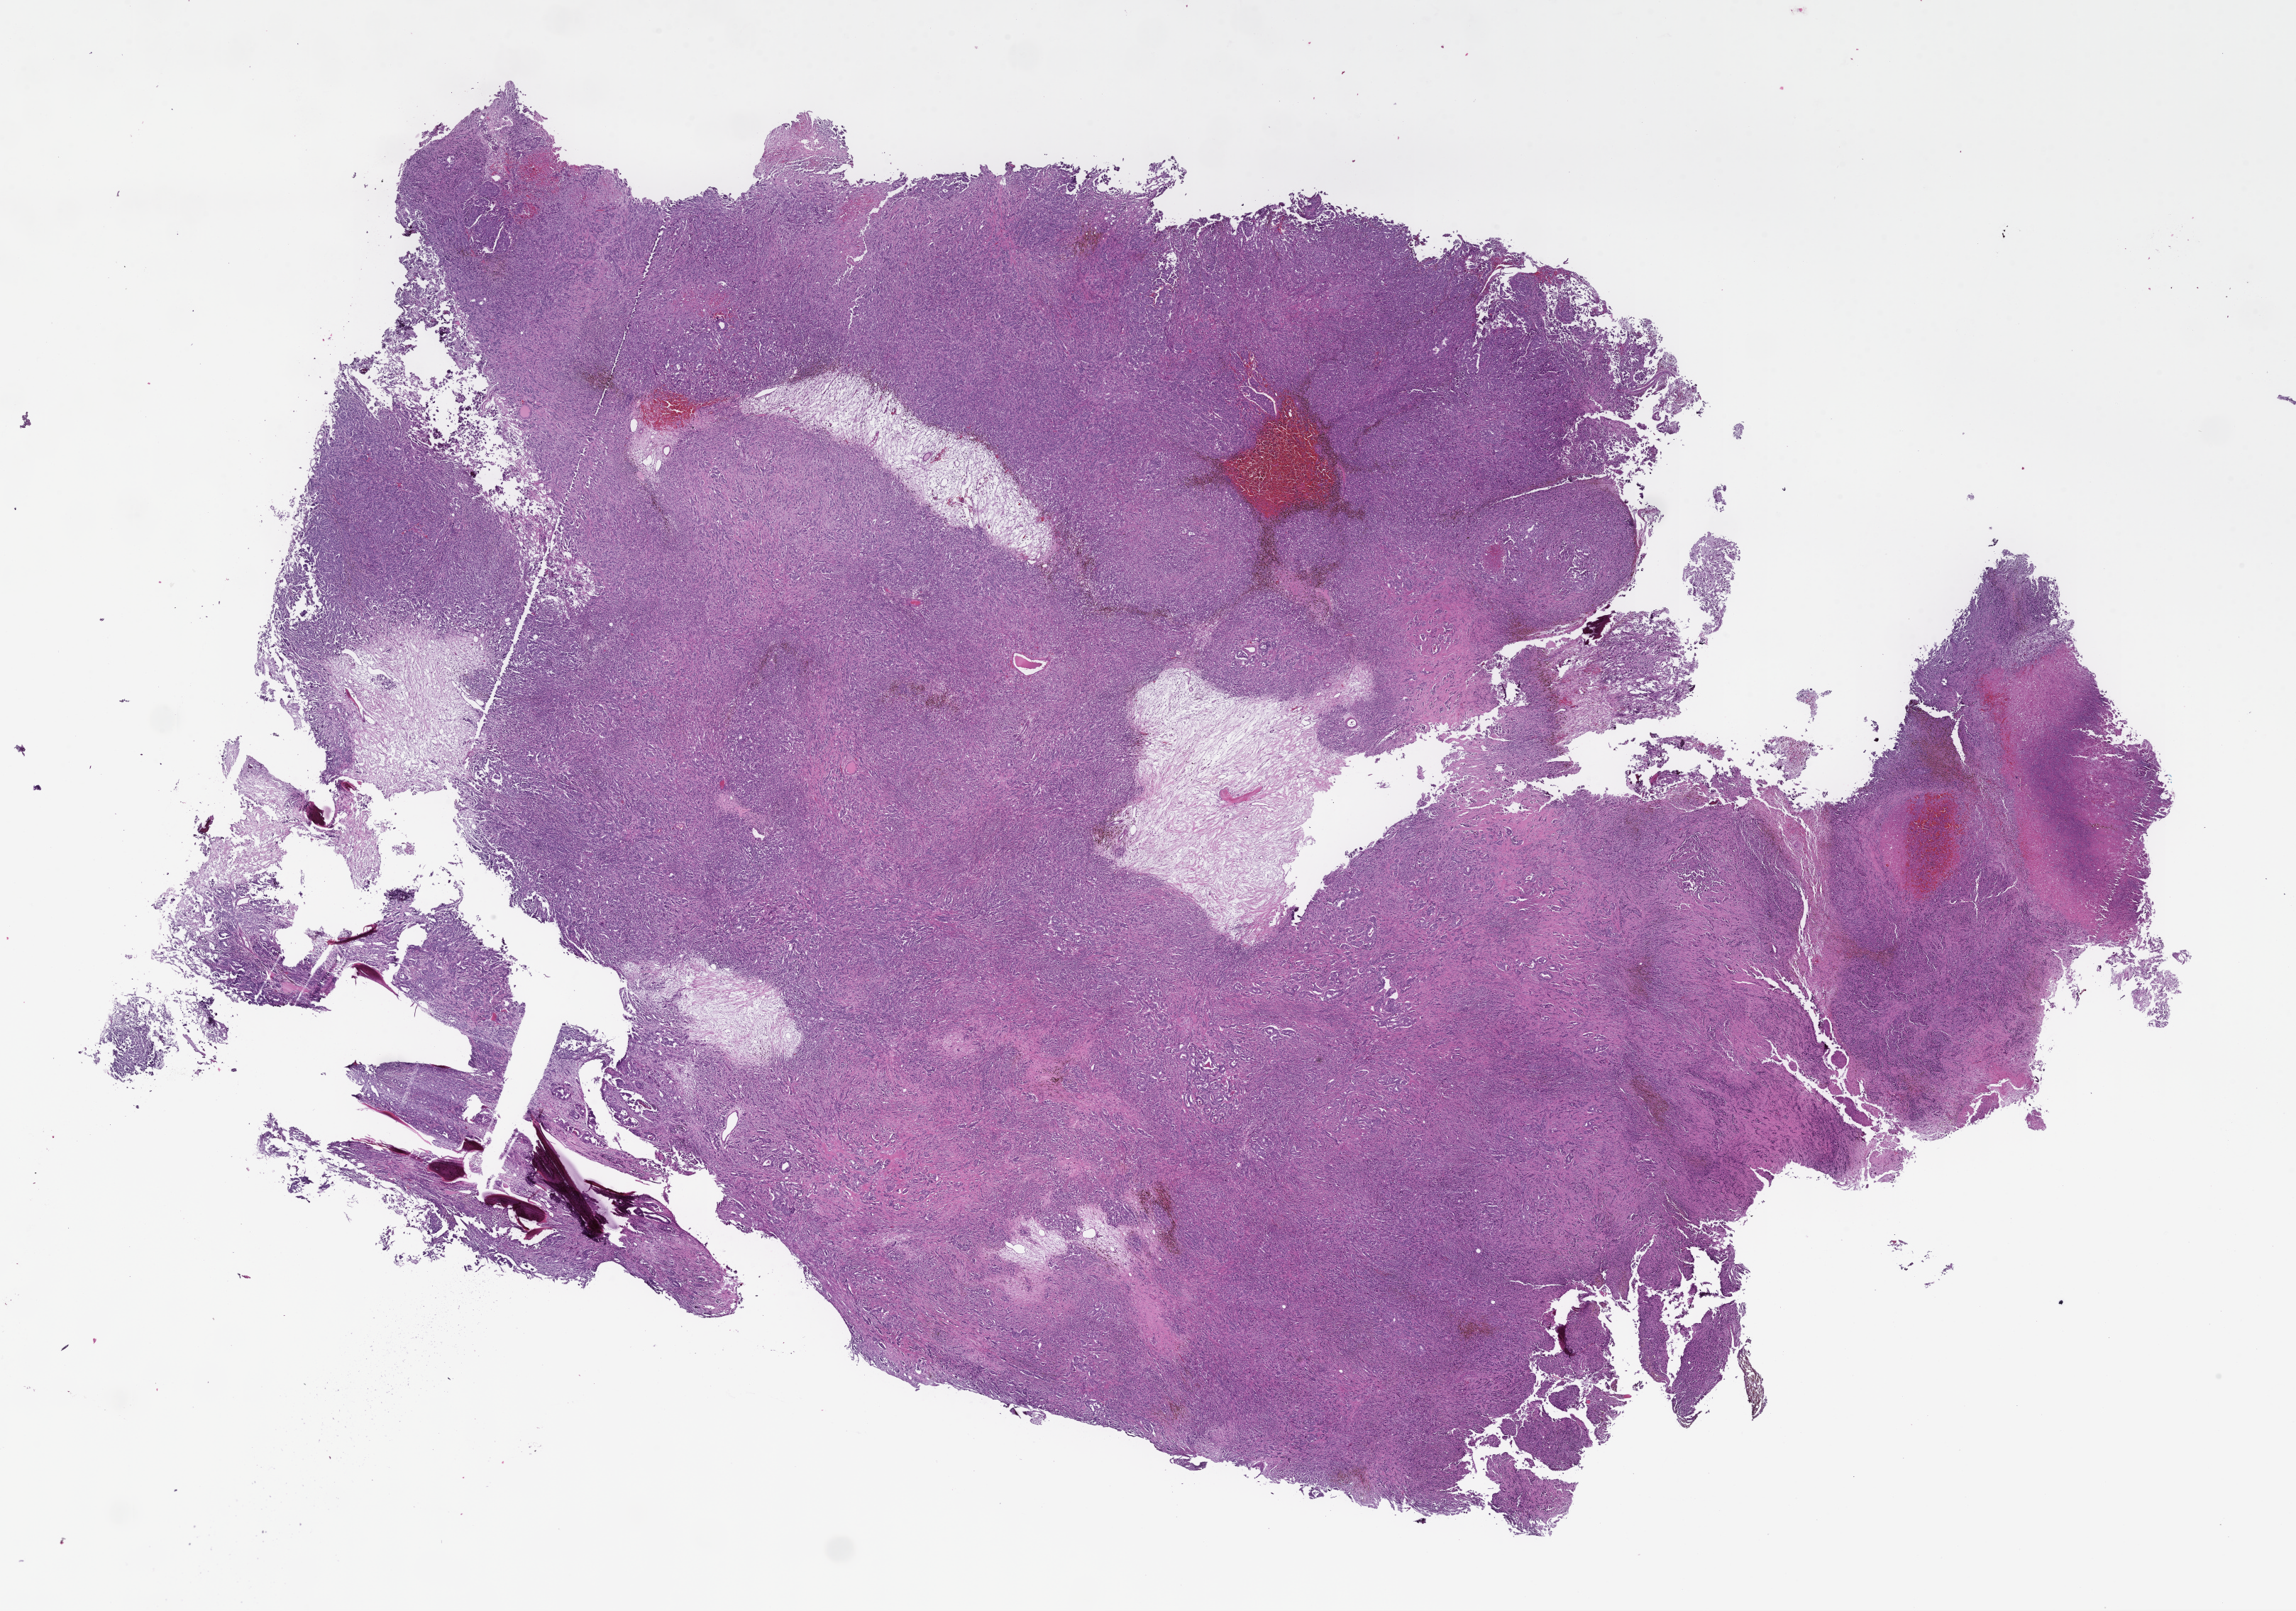
Hematoxylin and eosin (H&E) whole-slide image, low-resolution overview of the scanned area, about 26.1 x 18.3 mm; formalin-fixed paraffin-embedded section; specimen time point: archival tissue. Female patient.
- this section: metastatic tumor tissue
- primary diagnosis of the patient: Invasive Breast Carcinoma